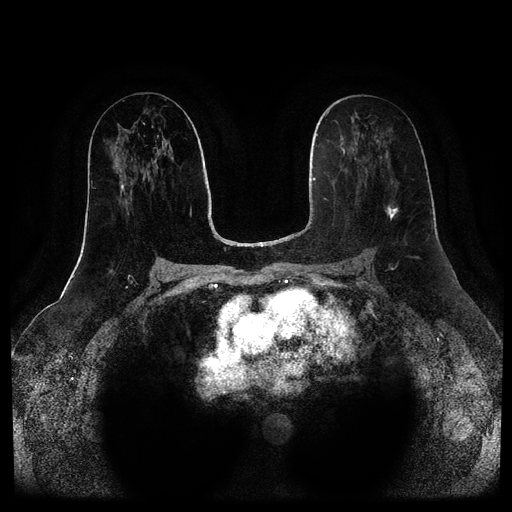
Breast MRI (dynamic contrast-enhanced, multi-phase), one axial slice; dynamic contrast-enhanced series, time point 2 of 5 at this slice position (early post-contrast); 1.5 T; TE 2.6 ms, TR 5.2 ms; 512 × 512 image matrix, field of view 380 × 380 mm. Female patient, age 57 years.
Outlined on this slice (semi-automatic segmentation, software-assisted and operator-edited):
- breast lesion (labelled 'tumour' in the annotation; benign lesions carry a separate 'benign' label): box from (x=387, y=206) to (x=399, y=220) px